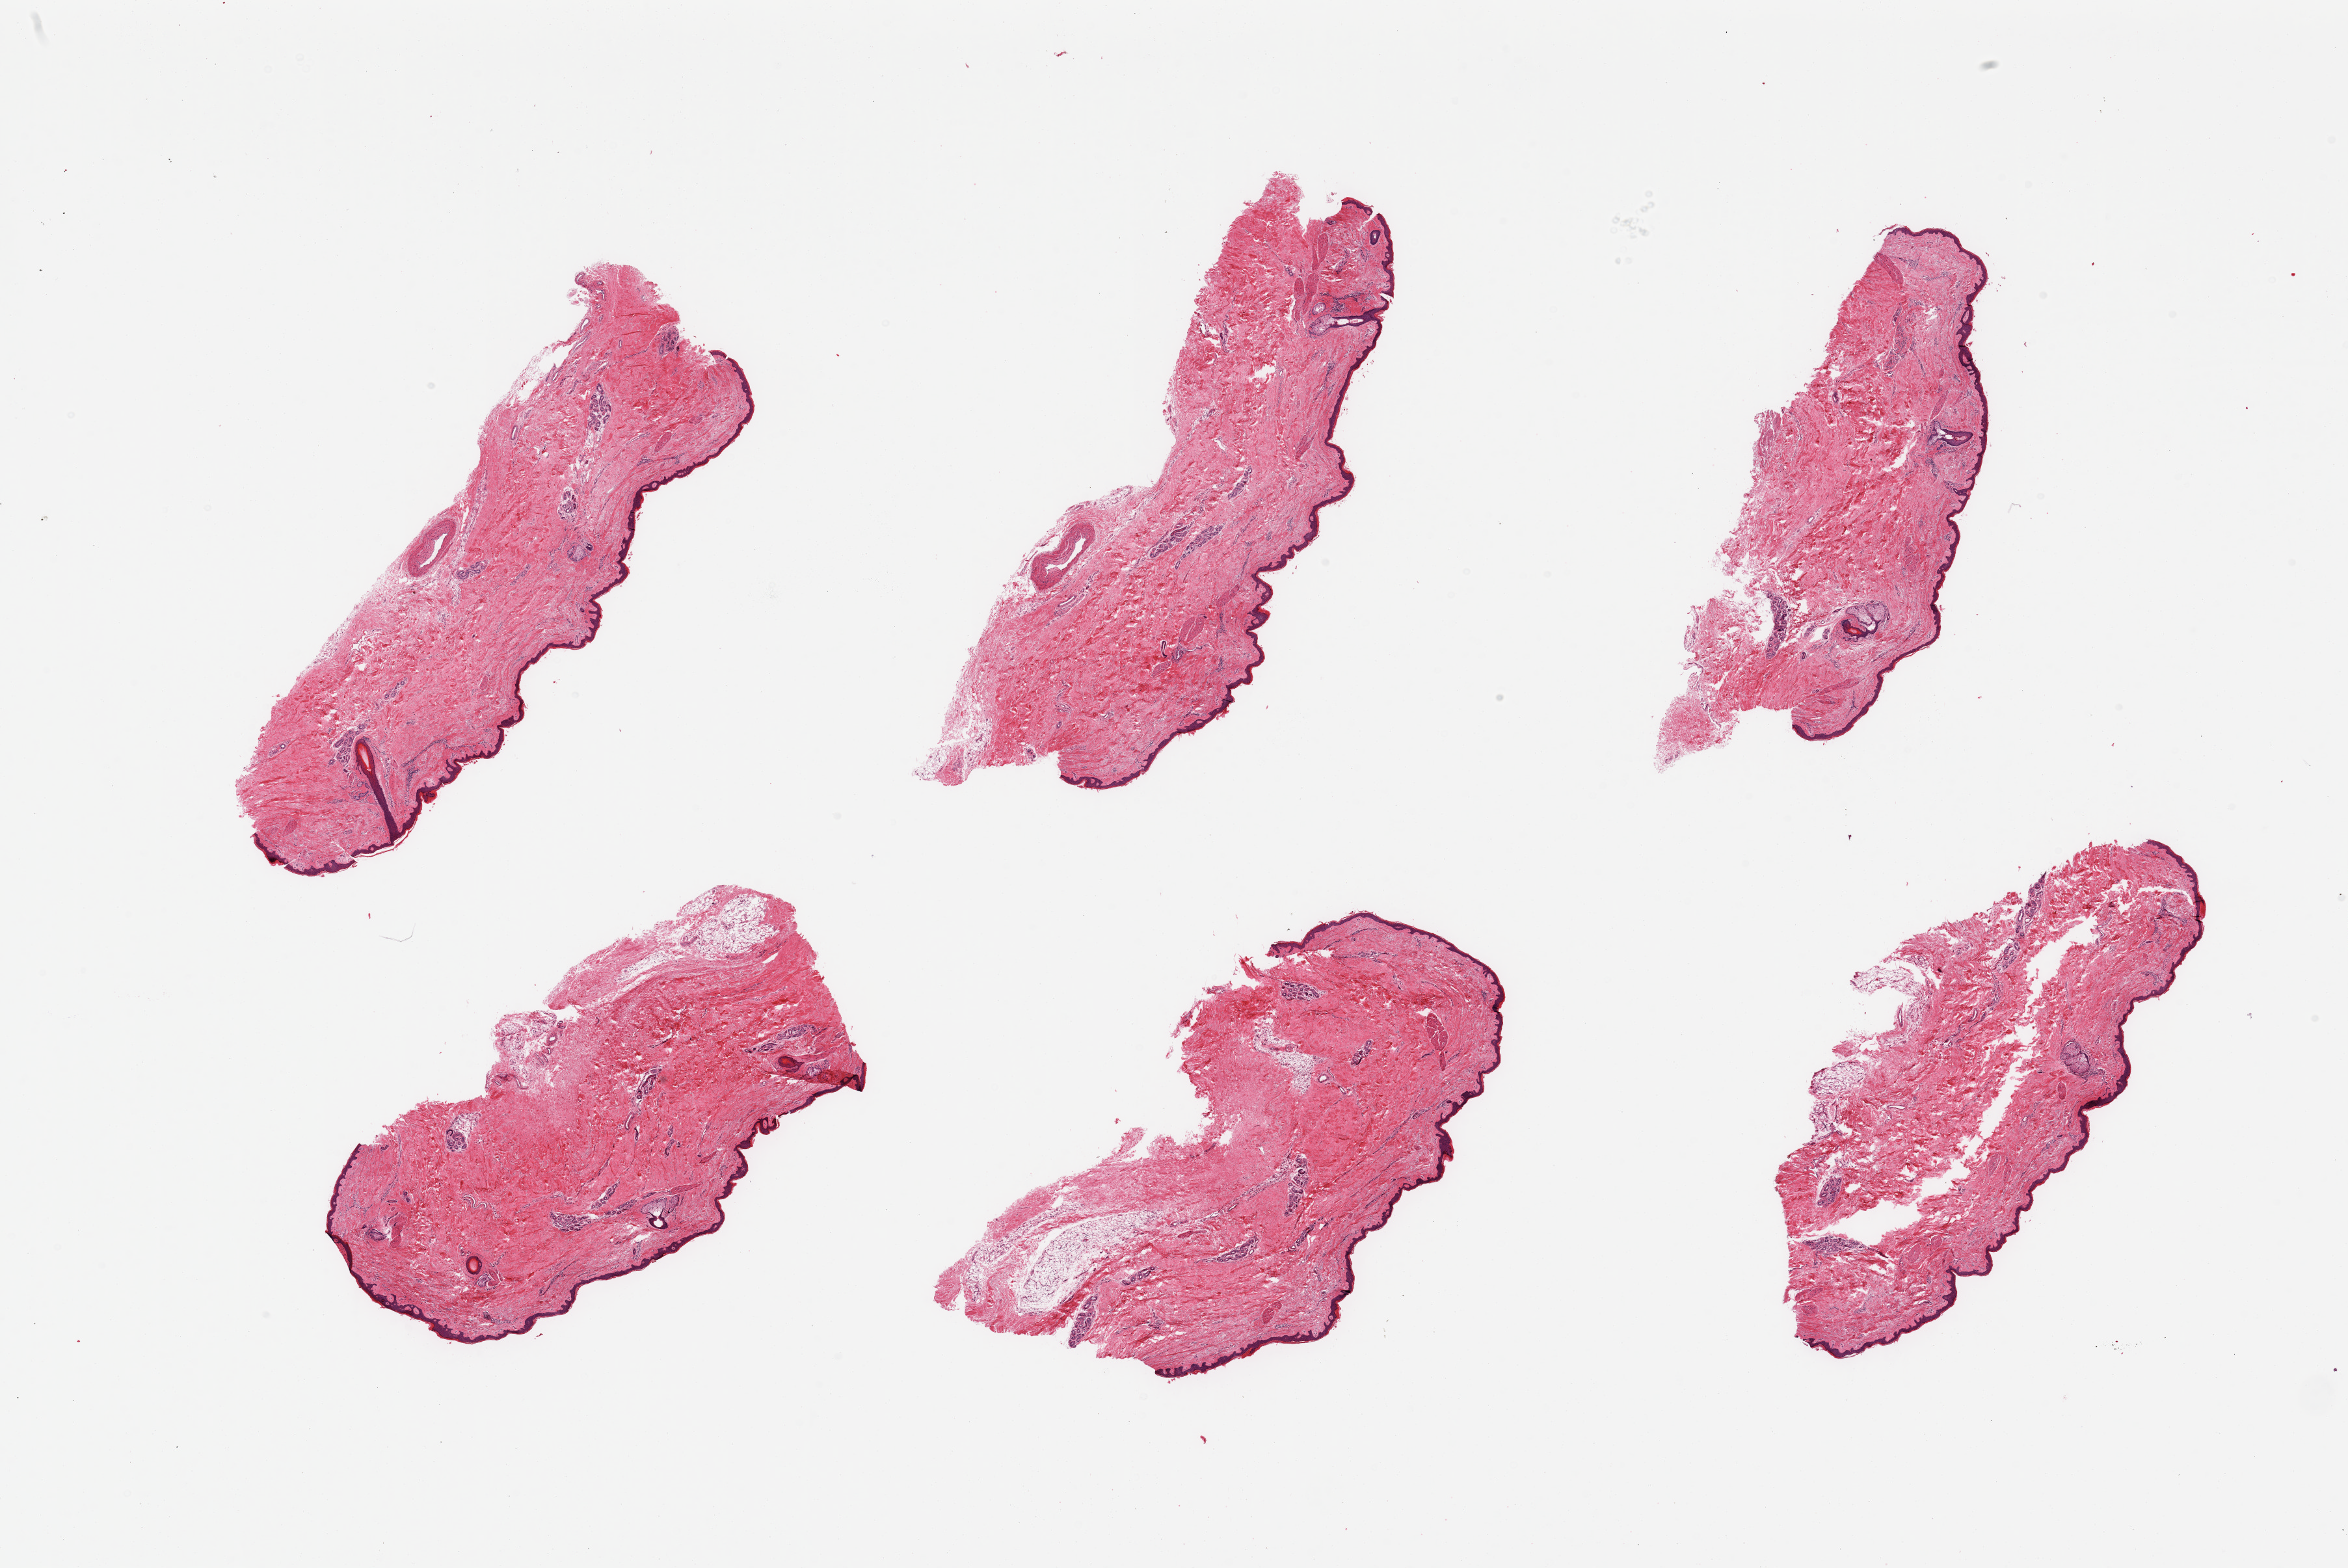
Whole-slide image, haematoxylin and eosin stain, a low-resolution overview of the entire scanned area, about 28.5 x 19.1 mm. PAXgene-fixed paraffin-embedded (PFPE) section. Target tissue: skin of lower leg. Tissue donor sample. Male donor.
• pathologist's review note for this sample: 6 pieces; well trimmed